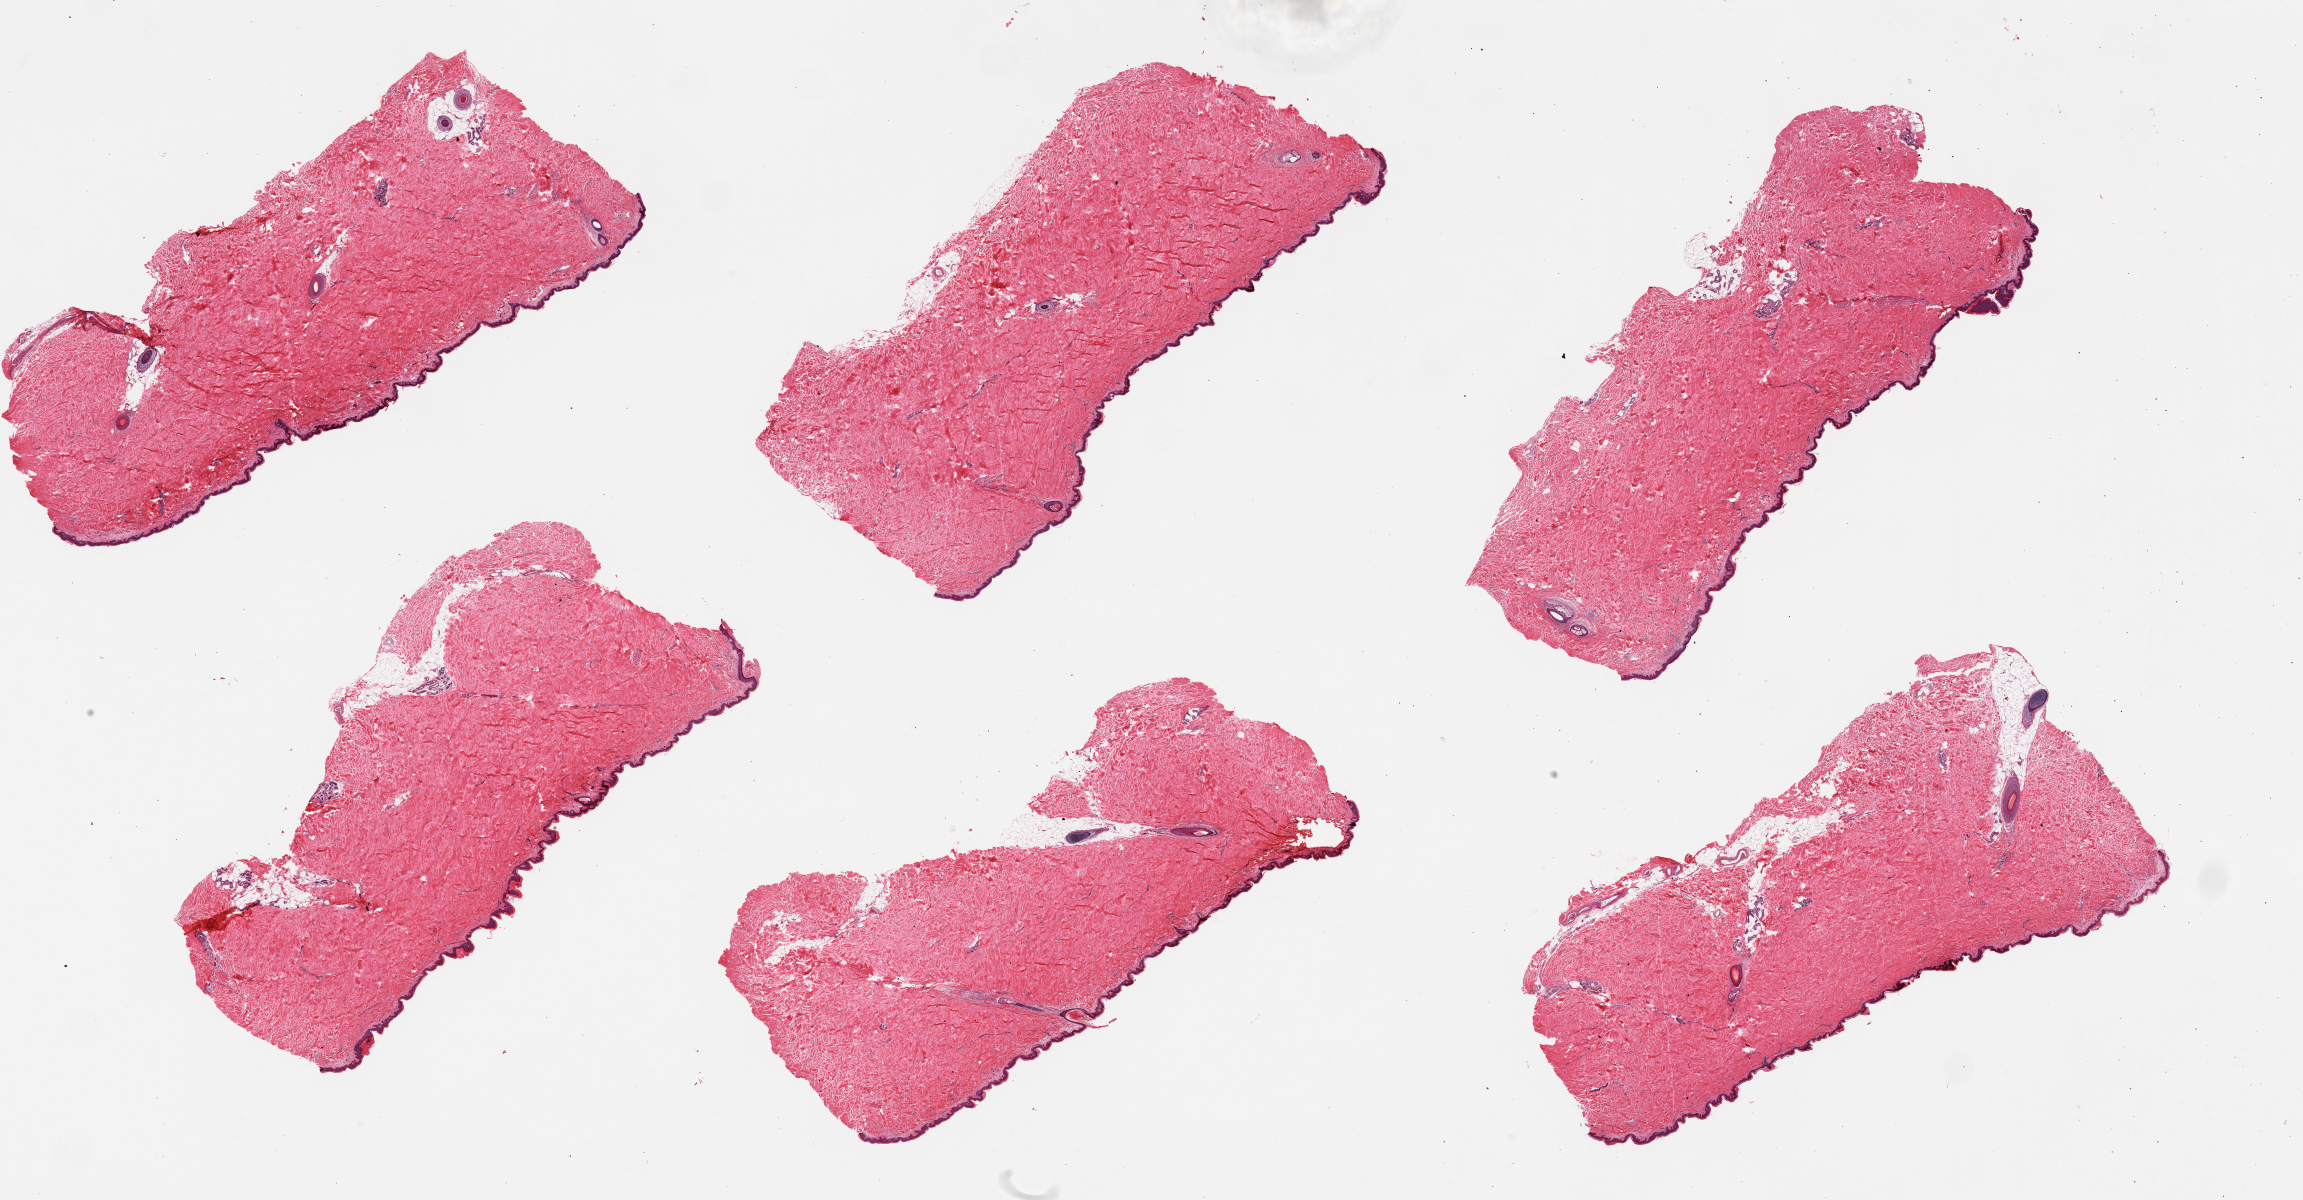
Whole-slide image, hematoxylin and eosin (H&E) stain, shown as a low-resolution overview of the whole scanned area (about 36.4 x 19.0 mm, from a 20x scan), PAXgene-fixed, paraffin-embedded tissue, section of skin of suprapubic region (target tissue), donor tissue sample. Donor sex: male.
• review note (as recorded): 6 pieces. Well trimmed of fat